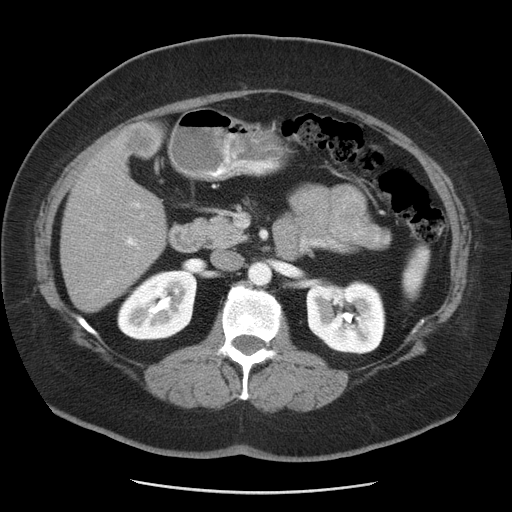
Contrast-enhanced abdominal CT, one axial slice; position 21 of 55 along the scan axis; reconstruction kernel STANDARD; intravenous contrast given; soft-tissue window (W 400 / L 40 HU); 5 mm slice thickness; 512 × 512 image matrix. Female patient, age 52 years. From the clinical record (not read from this slice): diagnosis: colorectal cancer liver metastases, imaged before liver resection; multiple liver metastases: yes; largest metastasis: 2.5 cm; disease in both lobes: yes.
Structures marked on this image (manually delineated by an expert):
- liver: bounding box (x1, y1, x2, y2) in pixels: (61, 122, 167, 311)
- planned liver remnant (the part of the liver to remain after resection): (61, 189, 167, 312)
- portal vein (with intrahepatic branches): (95, 186, 144, 282)
- liver metastasis: (122, 127, 158, 153)